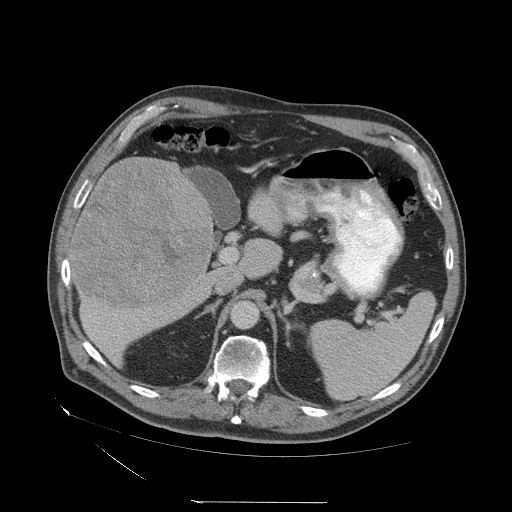
Contrast-enhanced abdominal CT (liver protocol), one axial slice; slice 30 of 83 in the series (ordered by position); 140 kVp; soft-tissue window (W 400 / L 40 HU); 512 × 512 image matrix. Case-level facts recorded for this patient, not image findings: diagnosis: hepatocellular carcinoma (patient treated with transarterial chemoembolisation; whether this scan precedes or follows treatment is not stated here); TNM stage (as recorded): Stage-I; Child-Pugh class: A; tumour differentiation: well differentiated.
Outlined on this slice (semi-automatic segmentation, software-assisted and operator-edited):
- liver parenchyma outside the tumour (the mass and vessels are separate outlines, so this box may not span the whole liver): bounding box [x1, y1, x2, y2] px = [68, 156, 214, 366]
- mass: [71, 157, 211, 307]